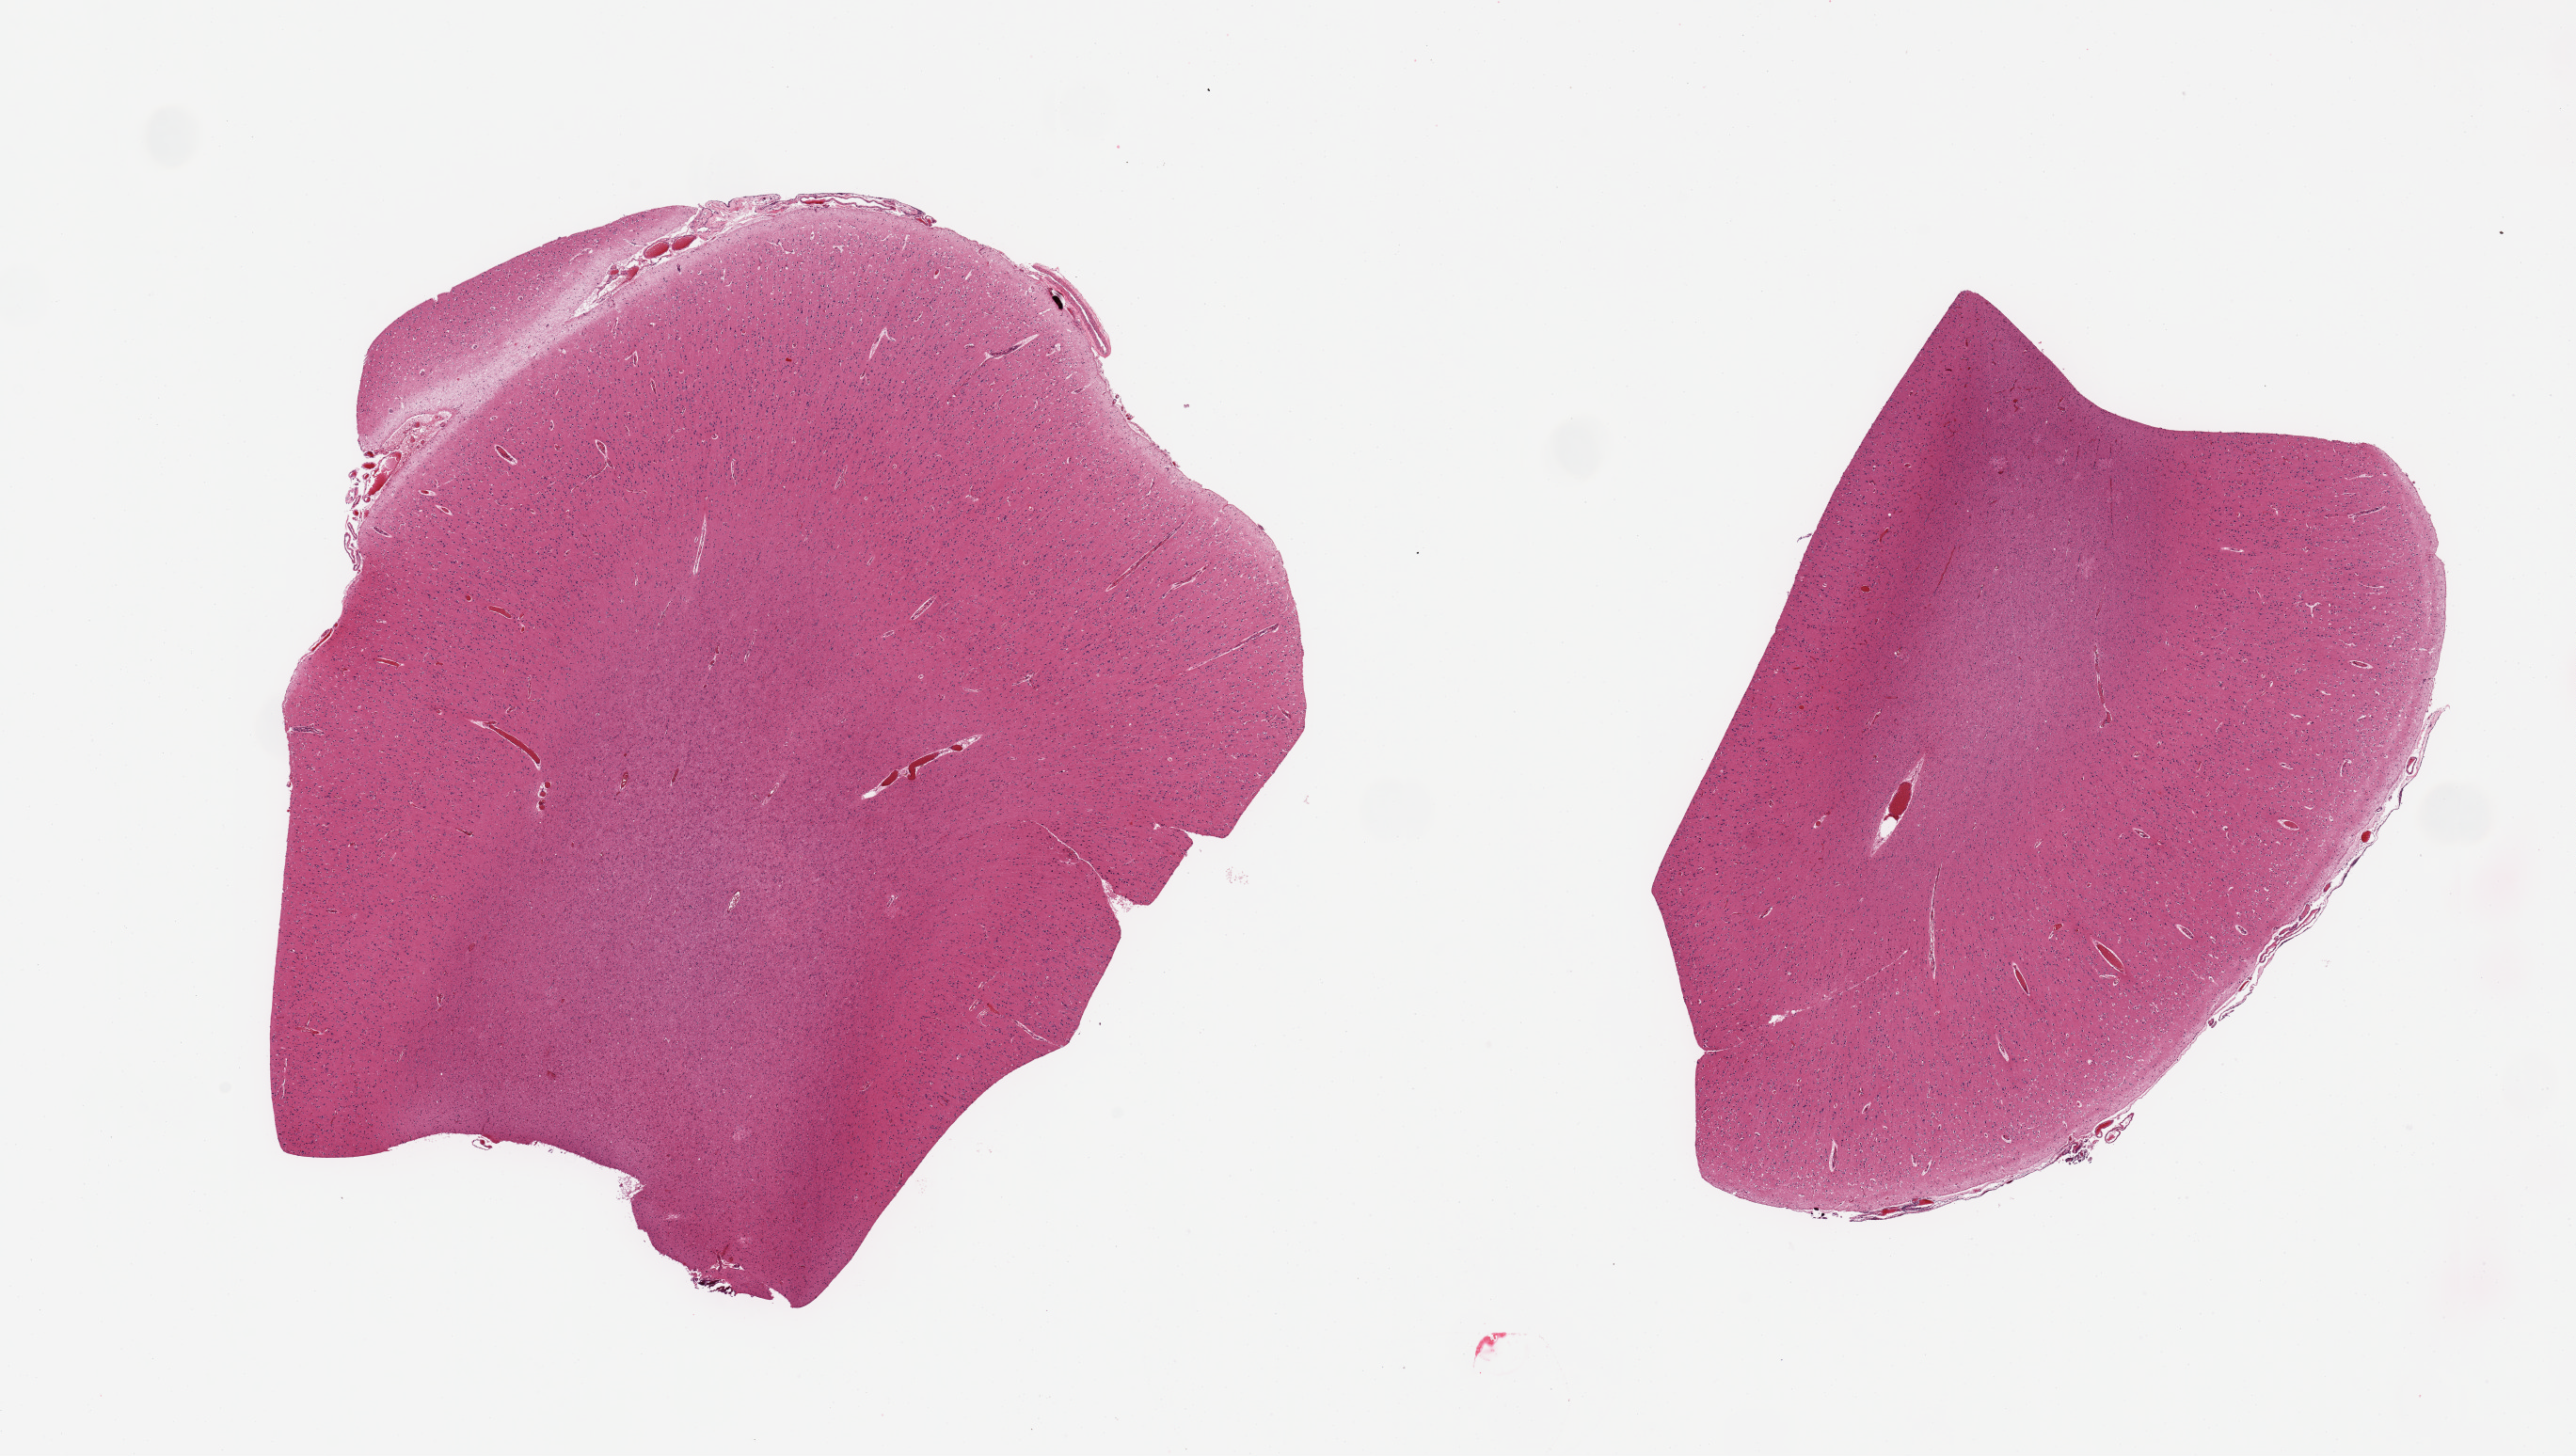
H&E whole-slide image — low-resolution overview of the scanned area, about 21.7 x 12.2 mm (from a 20x scan); PAXgene-fixed, paraffin-embedded tissue; sampled site (target tissue): cerebral cortex; tissue donor sample. Donor sex: male.
• reviewer comment on this tissue sample: 2 pieces, no abnormalites